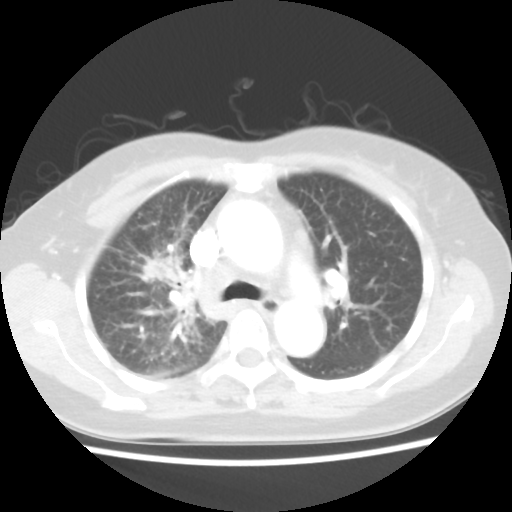
Chest CT, one axial slice. Slice 30 of 48 in the series (ordered by position). 100 kVp. Lung window (W 1500 / L -600 HU). 5 mm slice thickness. 512 × 512 image matrix, field of view 312 × 312 mm. Patient: female, 55 years. Case-level facts recorded for this patient, not image findings: clinical TNM (as recorded): T1b N3 M1a.
Annotated regions visible in this slice (bounding box drawn by a radiologist):
- lung tumour (recorded histology: adenocarcinoma): bounding box <140,258,184,283> (left, top, right, bottom; pixels)